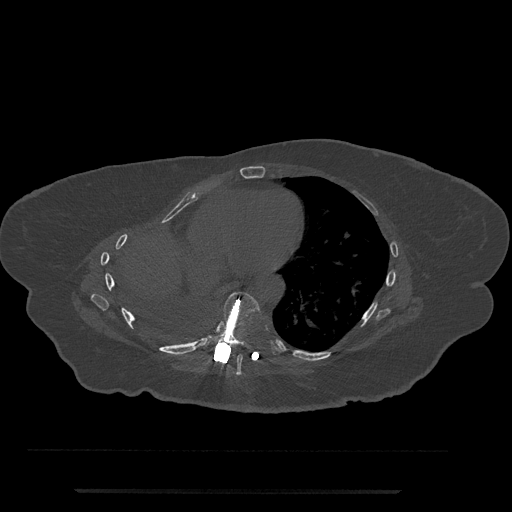
CT including the spine, one axial slice; position 404 of 797 along the scan axis; 120 kVp; bone window (W 1800 / L 400 HU); 0.5 mm slice thickness; 512 × 512 image matrix, field of view 440 × 440 mm. Female patient, age 51 years. From the clinical record (not read from this slice): primary cancer: neuro.
Structures marked on this image (semi-automatic segmentation, software-assisted and operator-edited):
- T7 vertebra: box from (x=203, y=354) to (x=243, y=375) px
- T8 vertebra: (x=203, y=292)–(x=261, y=351)